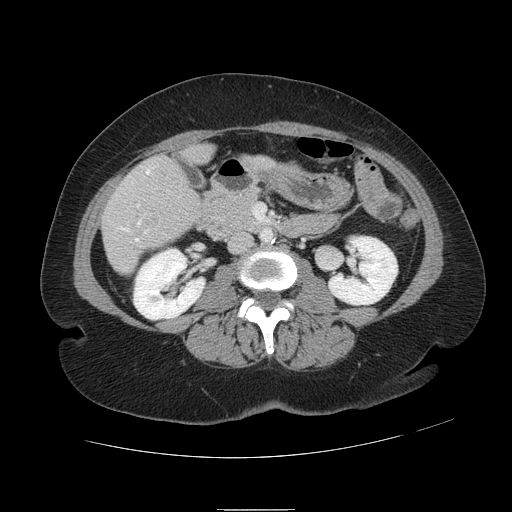
Contrast-enhanced abdominal CT, one axial slice; position 27 of 121 along the scan axis; intravenous contrast given; soft-tissue window (W 400 / L 40 HU); 2.5 mm slice thickness; 512 × 512 image matrix, field of view 400 × 400 mm. Female patient, age 52 years. From the clinical record (not read from this slice): diagnosis: colorectal cancer liver metastases, imaged before liver resection; multiple liver metastases: yes; largest metastasis: 6.3 cm; disease in both lobes: no.
Annotated regions visible in this slice (expert manual segmentation):
- hepatic veins: bounding box (x1, y1, x2, y2) in pixels: (119, 171, 150, 241)
- liver: (102, 146, 212, 274)
- planned liver remnant (the part of the liver to remain after resection): (187, 147, 212, 163)
- portal vein (with intrahepatic branches): (137, 204, 140, 207)